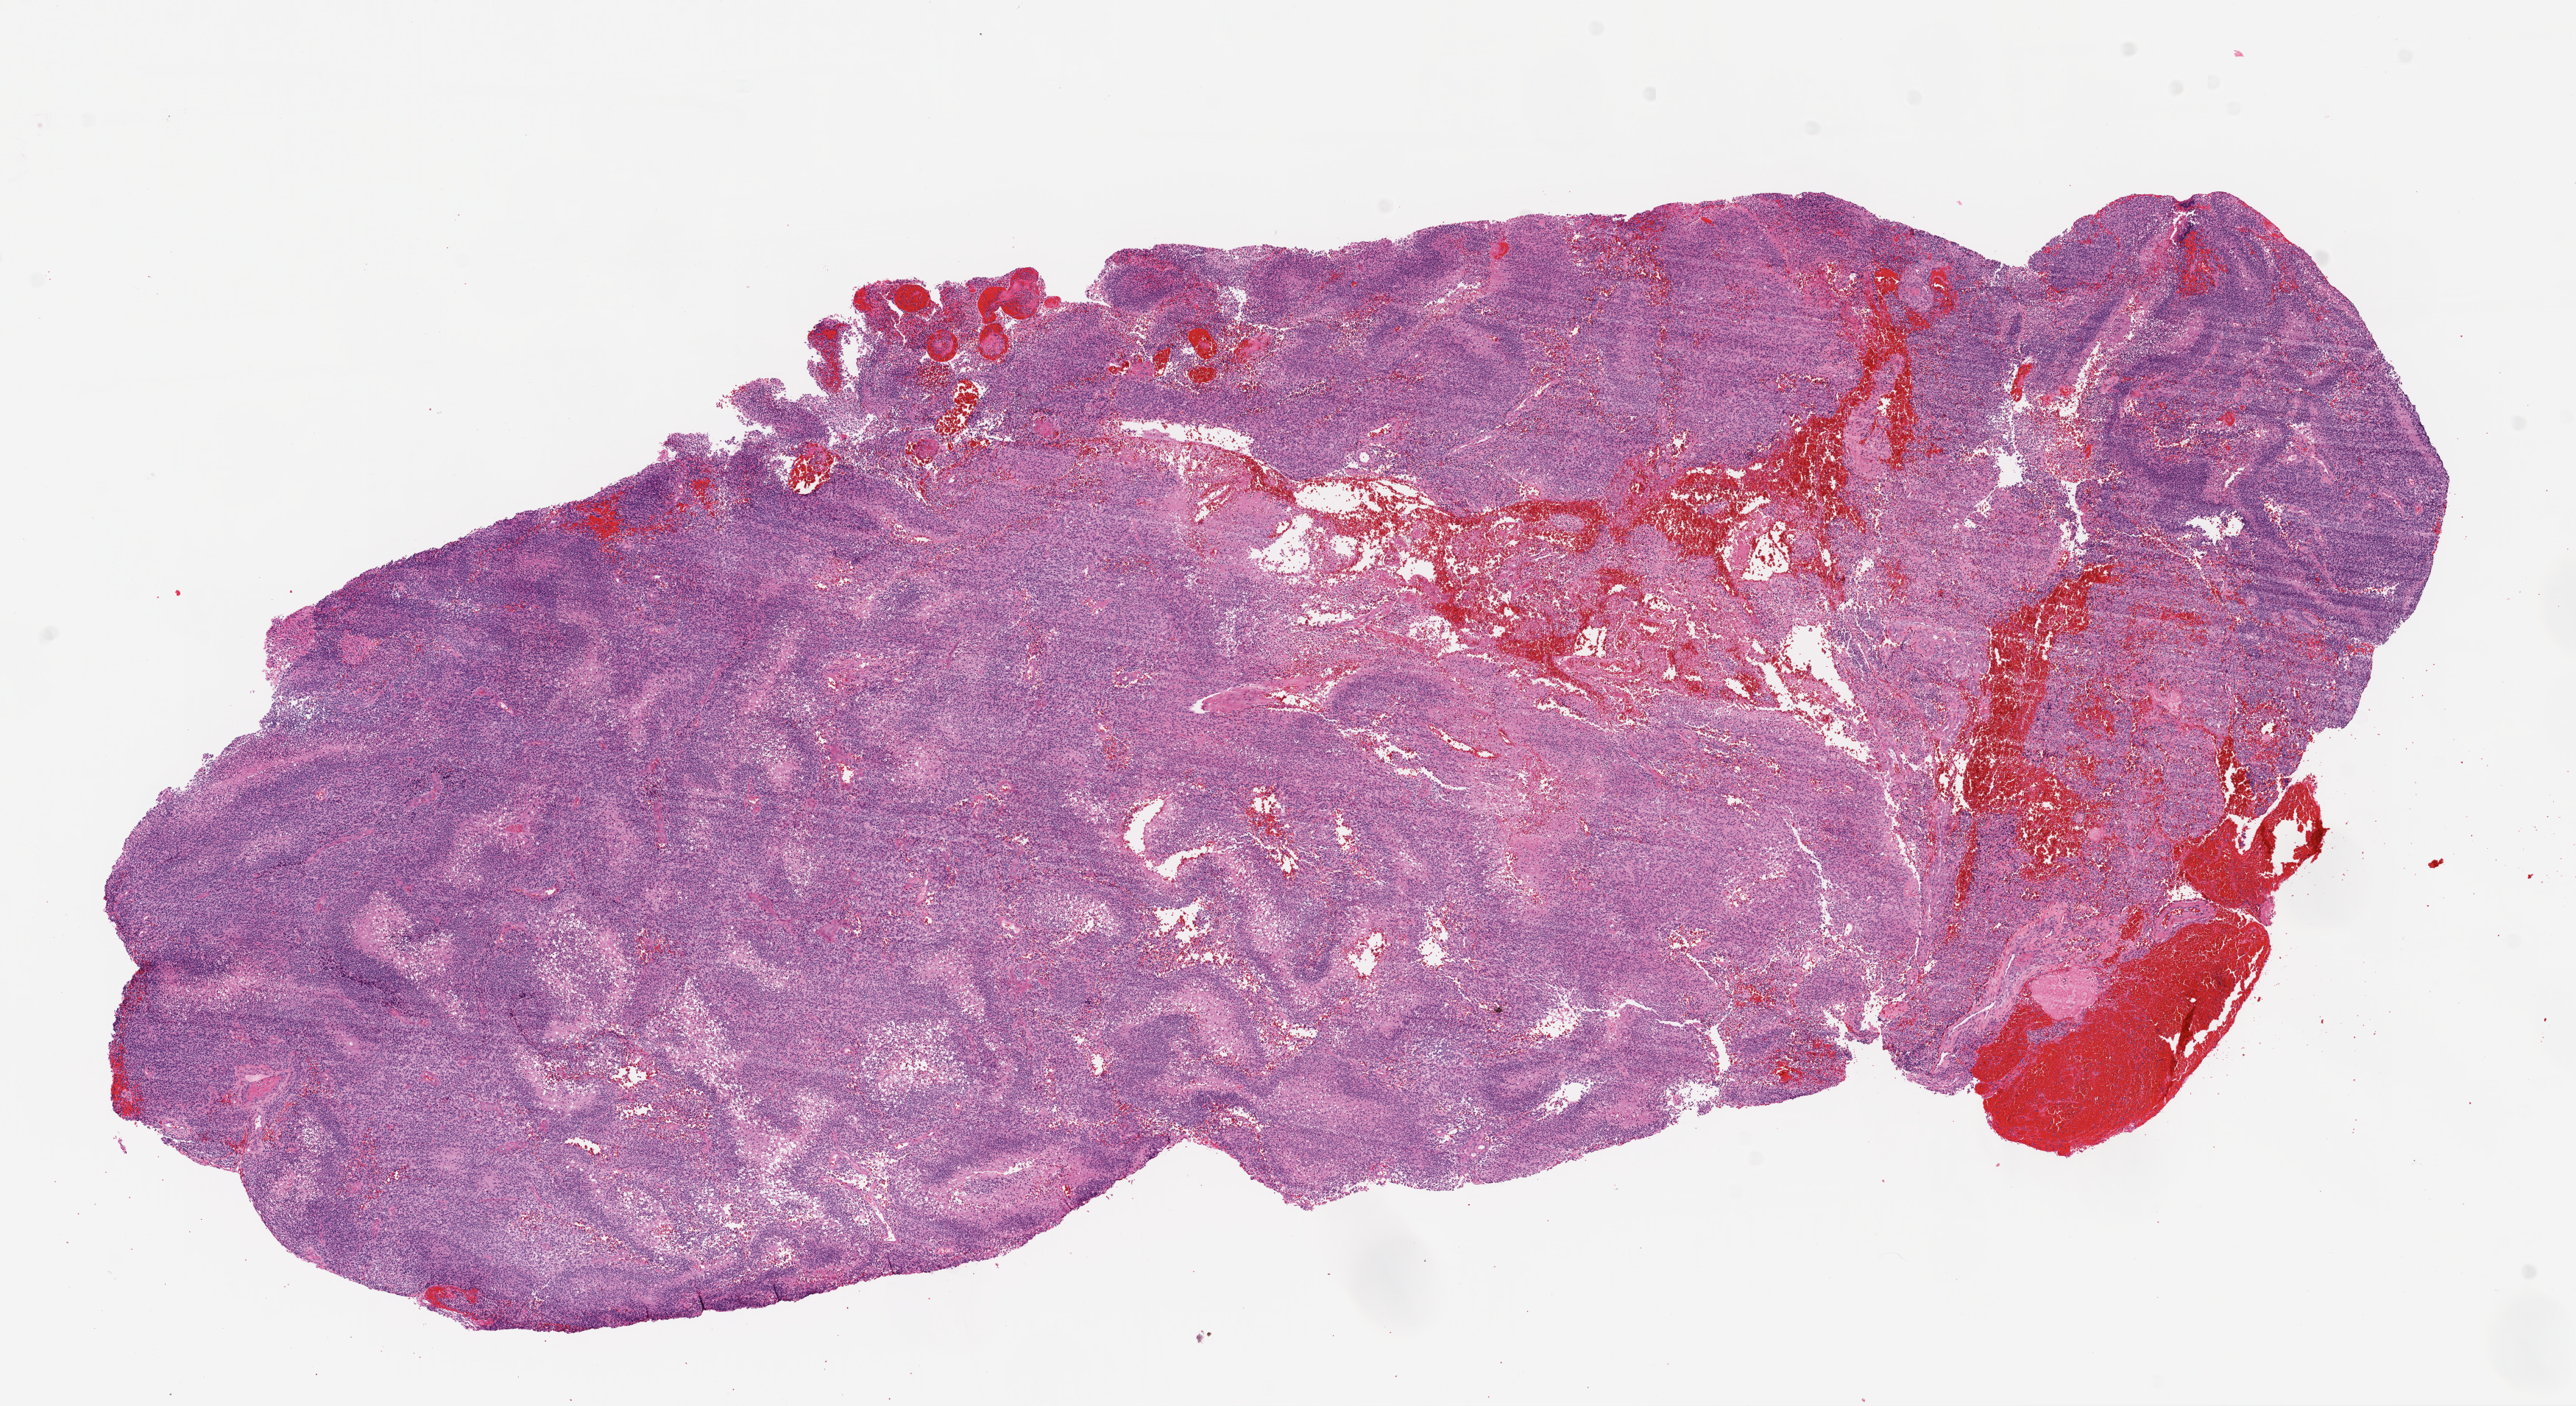
H&E-stained whole-slide image, shown as a low-resolution overview of the whole scanned area (about 14.0 x 7.7 mm, slide scanned at 20x); formalin-fixed paraffin-embedded (FFPE) diagnostic section; brain, primary tumour sample. Female, age 52 years at initial diagnosis.
Diagnosis: Glioblastoma.